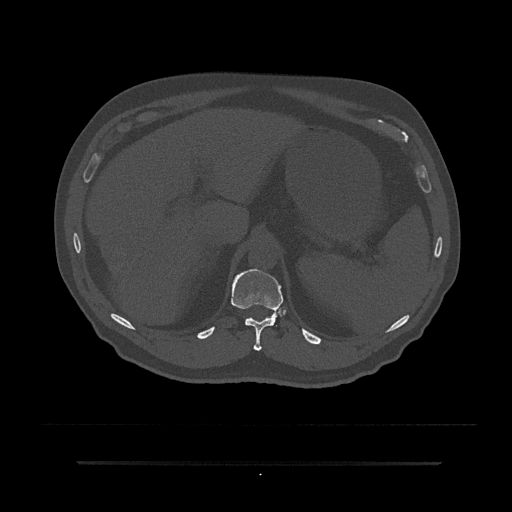
CT including the spine, one axial slice. Slice 259 of 797 in the series (ordered by position). Reconstruction kernel Br40s/3. 120 kVp. Bone window (W 1800 / L 400 HU). 0.5 mm slice thickness. 512 × 512 image matrix, field of view 464 × 464 mm. Male patient, age 59 years. Case-level facts recorded for this patient, not image findings: primary cancer: bile ducts.
Structures marked on this image (semi-automatically segmented with operator editing):
- T11 vertebra: box from (x=231, y=269) to (x=285, y=351) px